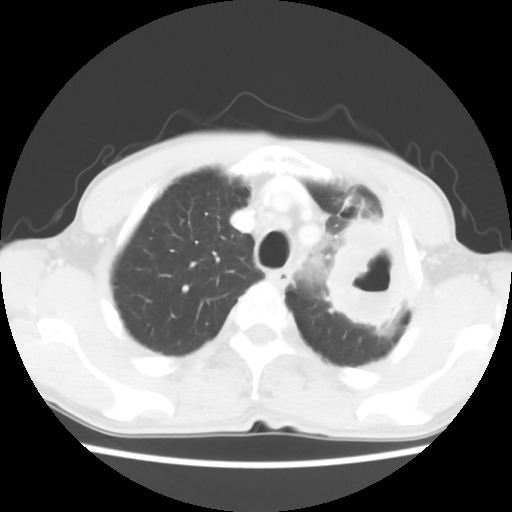
Chest CT, one axial slice; slice 48 of 60 in the series (ordered by position); 120 kVp; lung window (W 1500 / L -600 HU); 5 mm slice thickness; 512 × 512 image matrix, field of view 308 × 308 mm. Male patient, age 64 years. From the clinical record (not read from this slice): clinical TNM (as recorded): T3 N3 M0; histopathological grade: G3.
Structures marked on this image (bounding box drawn by a radiologist):
- lung tumour (recorded histology: adenocarcinoma): bounding box <317,211,418,345> (left, top, right, bottom; pixels)